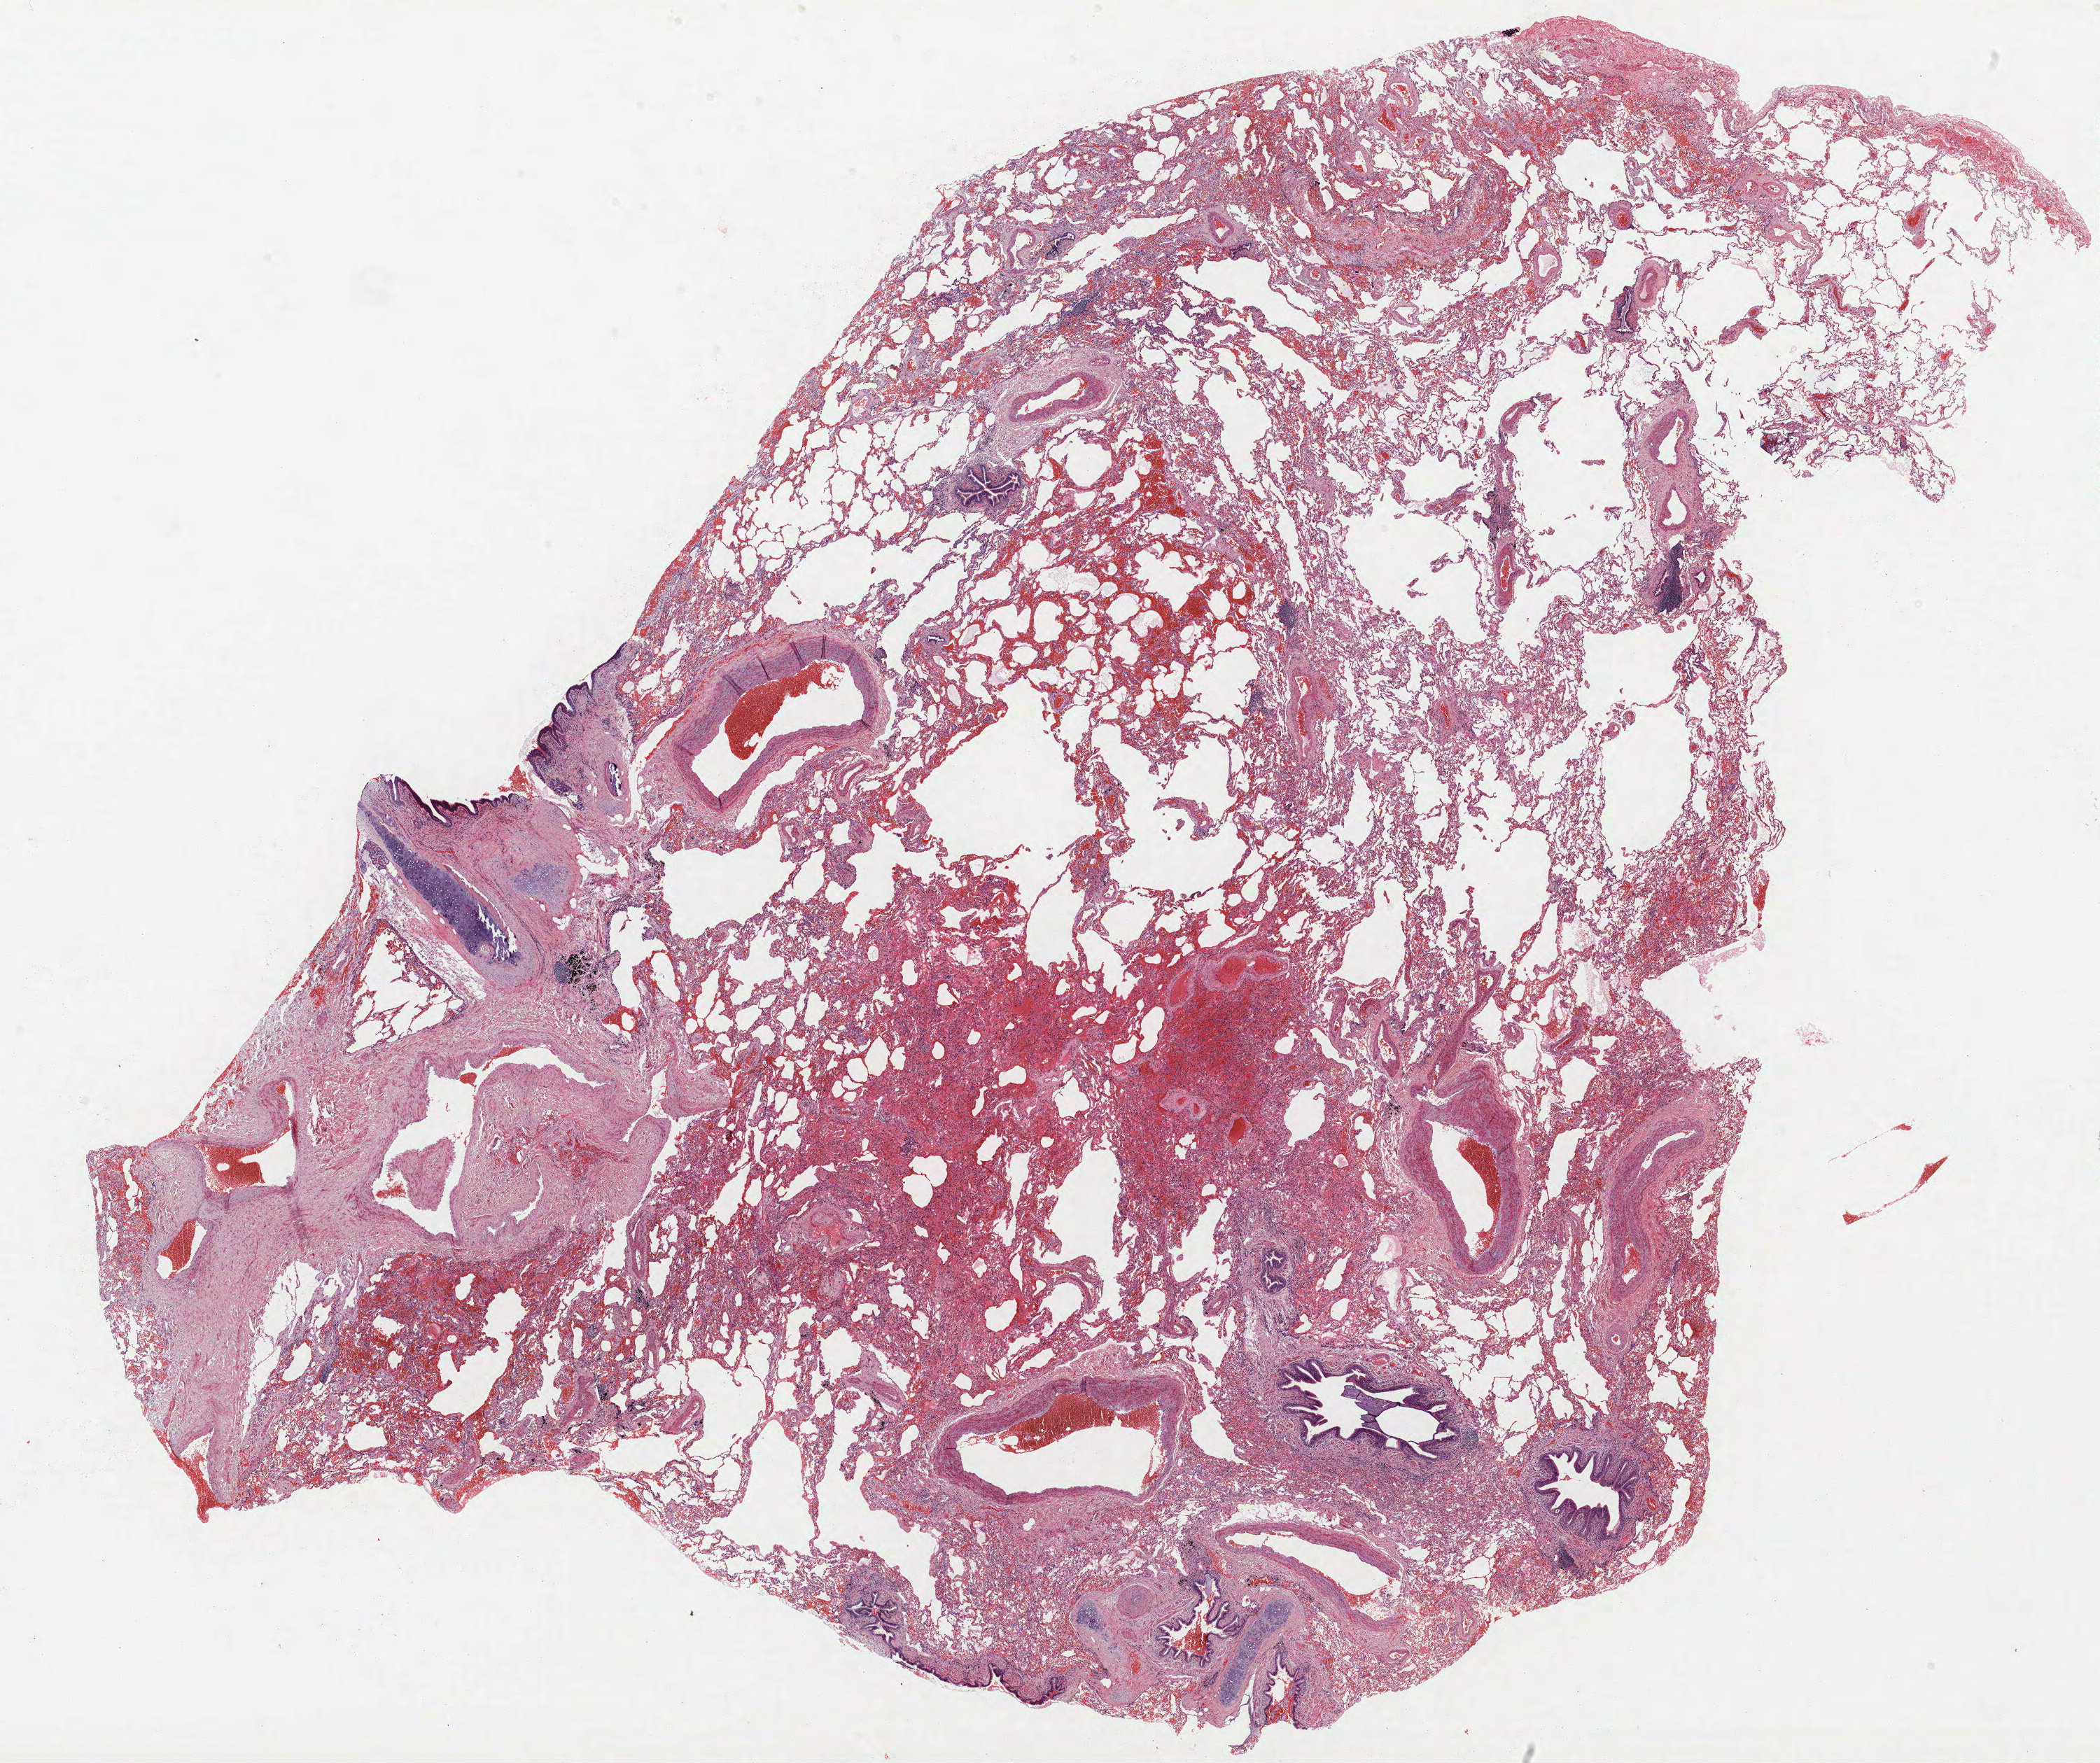
H&E whole-slide image — shown as a low-resolution overview of the whole scanned area (about 24.0 x 20.2 mm), formalin-fixed paraffin-embedded (FFPE) section, lung tissue. Male, age 64 at enrolment. Grade: poorly differentiated (G3).
Primary tumour location (clinical record): left upper lobe. Stage (AJCC 6th edition): IIA. Tumour size (pathology): 9 mm. Participant's lung-cancer diagnosis: Adenocarcinoma, NOS (ICD-O-3 8140/3).